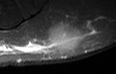
MRI of an extremity soft-tissue mass, one axial slice; slice 26 of 36 in the series (ordered by position); STIR; MR volume resampled by the dataset authors to the PET/CT grid (not the native acquisition matrix); 3.27 mm slice thickness; 116 × 74 image matrix, field of view 113 × 72 mm. Male patient. Case-level facts recorded for this patient, not image findings: histological type: pleiomorphic leiomyosarcoma; grade: high; site of the primary tumour: left buttock.
Outlined on this slice (expert contour drawn on MRI and transferred to this co-registered scan by the dataset authors):
- gross tumour volume including surrounding oedema: bounding box [x1, y1, x2, y2] px = [46, 26, 65, 52]
- gross tumour volume (mass): [48, 30, 65, 50]